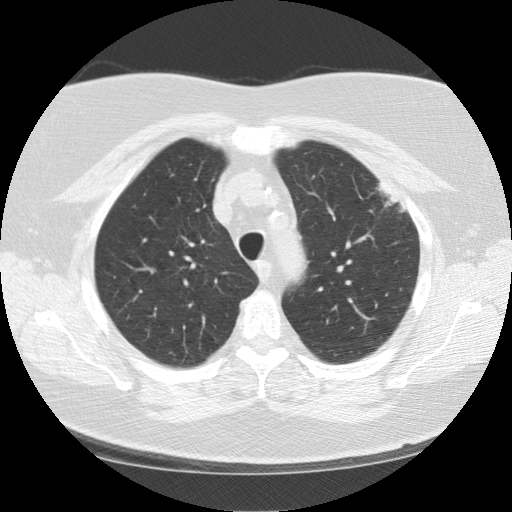
Chest CT (low-dose screening protocol), one axial image, baseline screening round, lung window (W 1500 / L -600 HU), 2.5 mm slice thickness, standard (soft-tissue) reconstruction kernel (STANDARD). Female participant, aged 67 years at enrolment.
Lesion marked by an expert reader, bounding box <351,166,420,227> (left, top, right, bottom; pixels). Reader record for this screening exam (exam-level; its link to the box is not recorded): non-calcified nodule or mass ≥4 mm, left upper lobe, 28 × 19 mm, soft tissue attenuation. Participant outcome: lung cancer diagnosed 33 days after this screen — squamous cell carcinoma, NOS, left upper lobe, poorly differentiated (G3), stage IA (AJCC 6th edition), 25 mm at pathology.